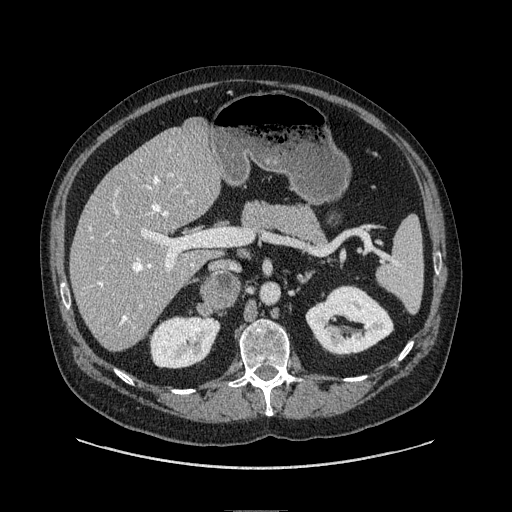
Contrast-enhanced abdominal CT, one axial slice; slice 43 of 149 in the series (ordered by position); soft-tissue window (W 400 / L 40 HU); 1.25 mm slice thickness; 512 × 512 image matrix, field of view 440 × 440 mm. Male patient. Case-level facts recorded for this patient, not image findings: diagnosis: adrenocortical carcinoma; tumour side: right adrenal; tumour size at pathology: 7.5 cm; Ki-67 index: 15 %; stage (as recorded): 2.
Annotated regions visible in this slice (semi-automatic segmentation, software-assisted and operator-edited):
- mass: bounding box [x1, y1, x2, y2] px = [205, 274, 238, 306]